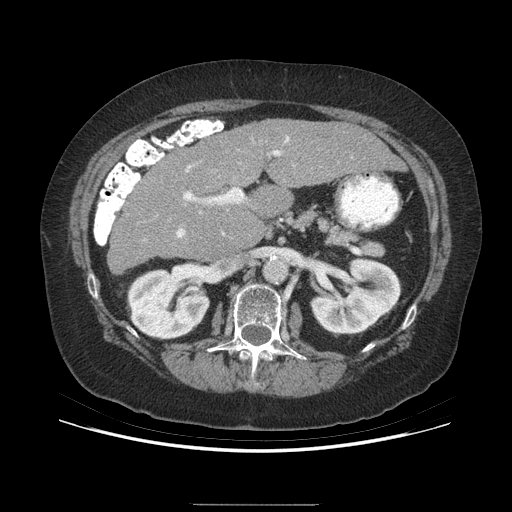
Contrast-enhanced abdominal CT (liver protocol), one axial slice. Slice 147 of 192 in the series (ordered by position). Soft-tissue window (W 400 / L 40 HU). 2.5 mm slice thickness. 512 × 512 image matrix, field of view 400 × 400 mm. Case-level facts recorded for this patient, not image findings: diagnosis: hepatocellular carcinoma (patient treated with transarterial chemoembolisation; whether this scan precedes or follows treatment is not stated here); TNM stage (as recorded): Stage-I; Child-Pugh class: A; tumour differentiation: moderately differentiated; tumour size: 3.2 cm.
Outlined on this slice (semi-automatic segmentation, software-assisted and operator-edited):
- liver parenchyma outside the tumour (the mass and vessels are separate outlines, so this box may not span the whole liver): bounding box (x1, y1, x2, y2) in pixels: (108, 118, 402, 270)
- liver vessels: (176, 137, 289, 237)